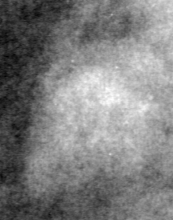
Crop from a digitized film mammogram around one marked abnormality, left breast, MLO view, BI-RADS breast density category 2 (scale 1–4).
Marked abnormality: mass, shape oval, margins circumscribed; BI-RADS assessment category 3; subtlety rating 4 on a 1 (subtle) to 5 (obvious) scale; pathology result (as recorded, not read from the image): benign.